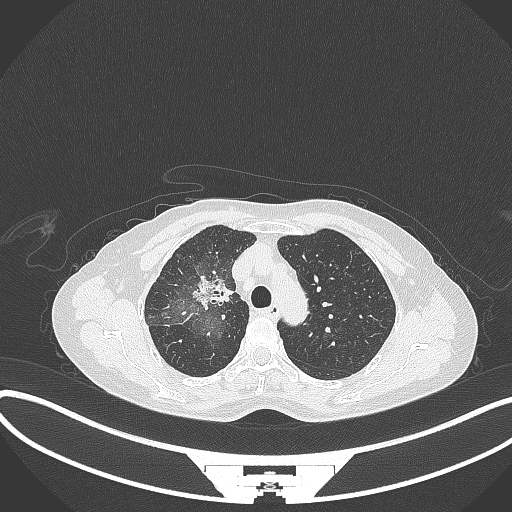
Chest CT, one axial slice; slice 236 of 284 in the series (ordered by position); lung window (W 1500 / L -600 HU); 512 × 512 image matrix, field of view 400 × 400 mm. Patient: female, 59 years. Case-level facts recorded for this patient, not image findings: clinical TNM (as recorded): T3 N0 M0; histopathological grade: G1.
Annotated regions visible in this slice (bounding box drawn by a radiologist):
- lung tumour (recorded histology: adenocarcinoma): box from (x=192, y=270) to (x=233, y=312) px